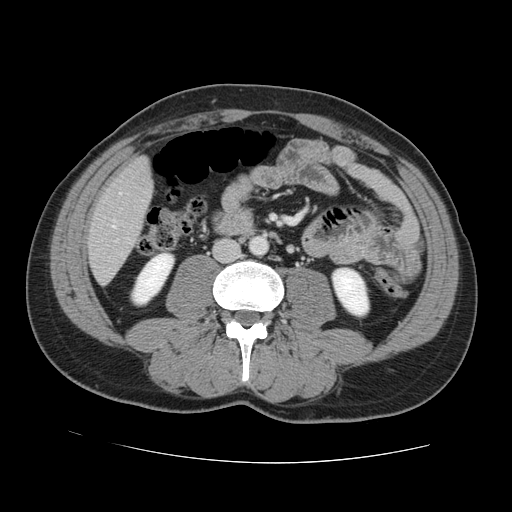
Contrast-enhanced abdominal CT, one axial slice. 120 kVp. Intravenous contrast given. Soft-tissue window (W 400 / L 40 HU). 512 × 512 image matrix, field of view 380 × 380 mm. Male patient, age 40 years. From the clinical record (not read from this slice): diagnosis: colorectal cancer liver metastases, imaged before liver resection; multiple liver metastases: yes; largest metastasis: 2.9 cm; disease in both lobes: yes.
Outlined on this slice (outlined manually by an expert reader):
- hepatic veins: box from (x=112, y=193) to (x=121, y=228) px
- liver: (x=90, y=159)–(x=151, y=282)